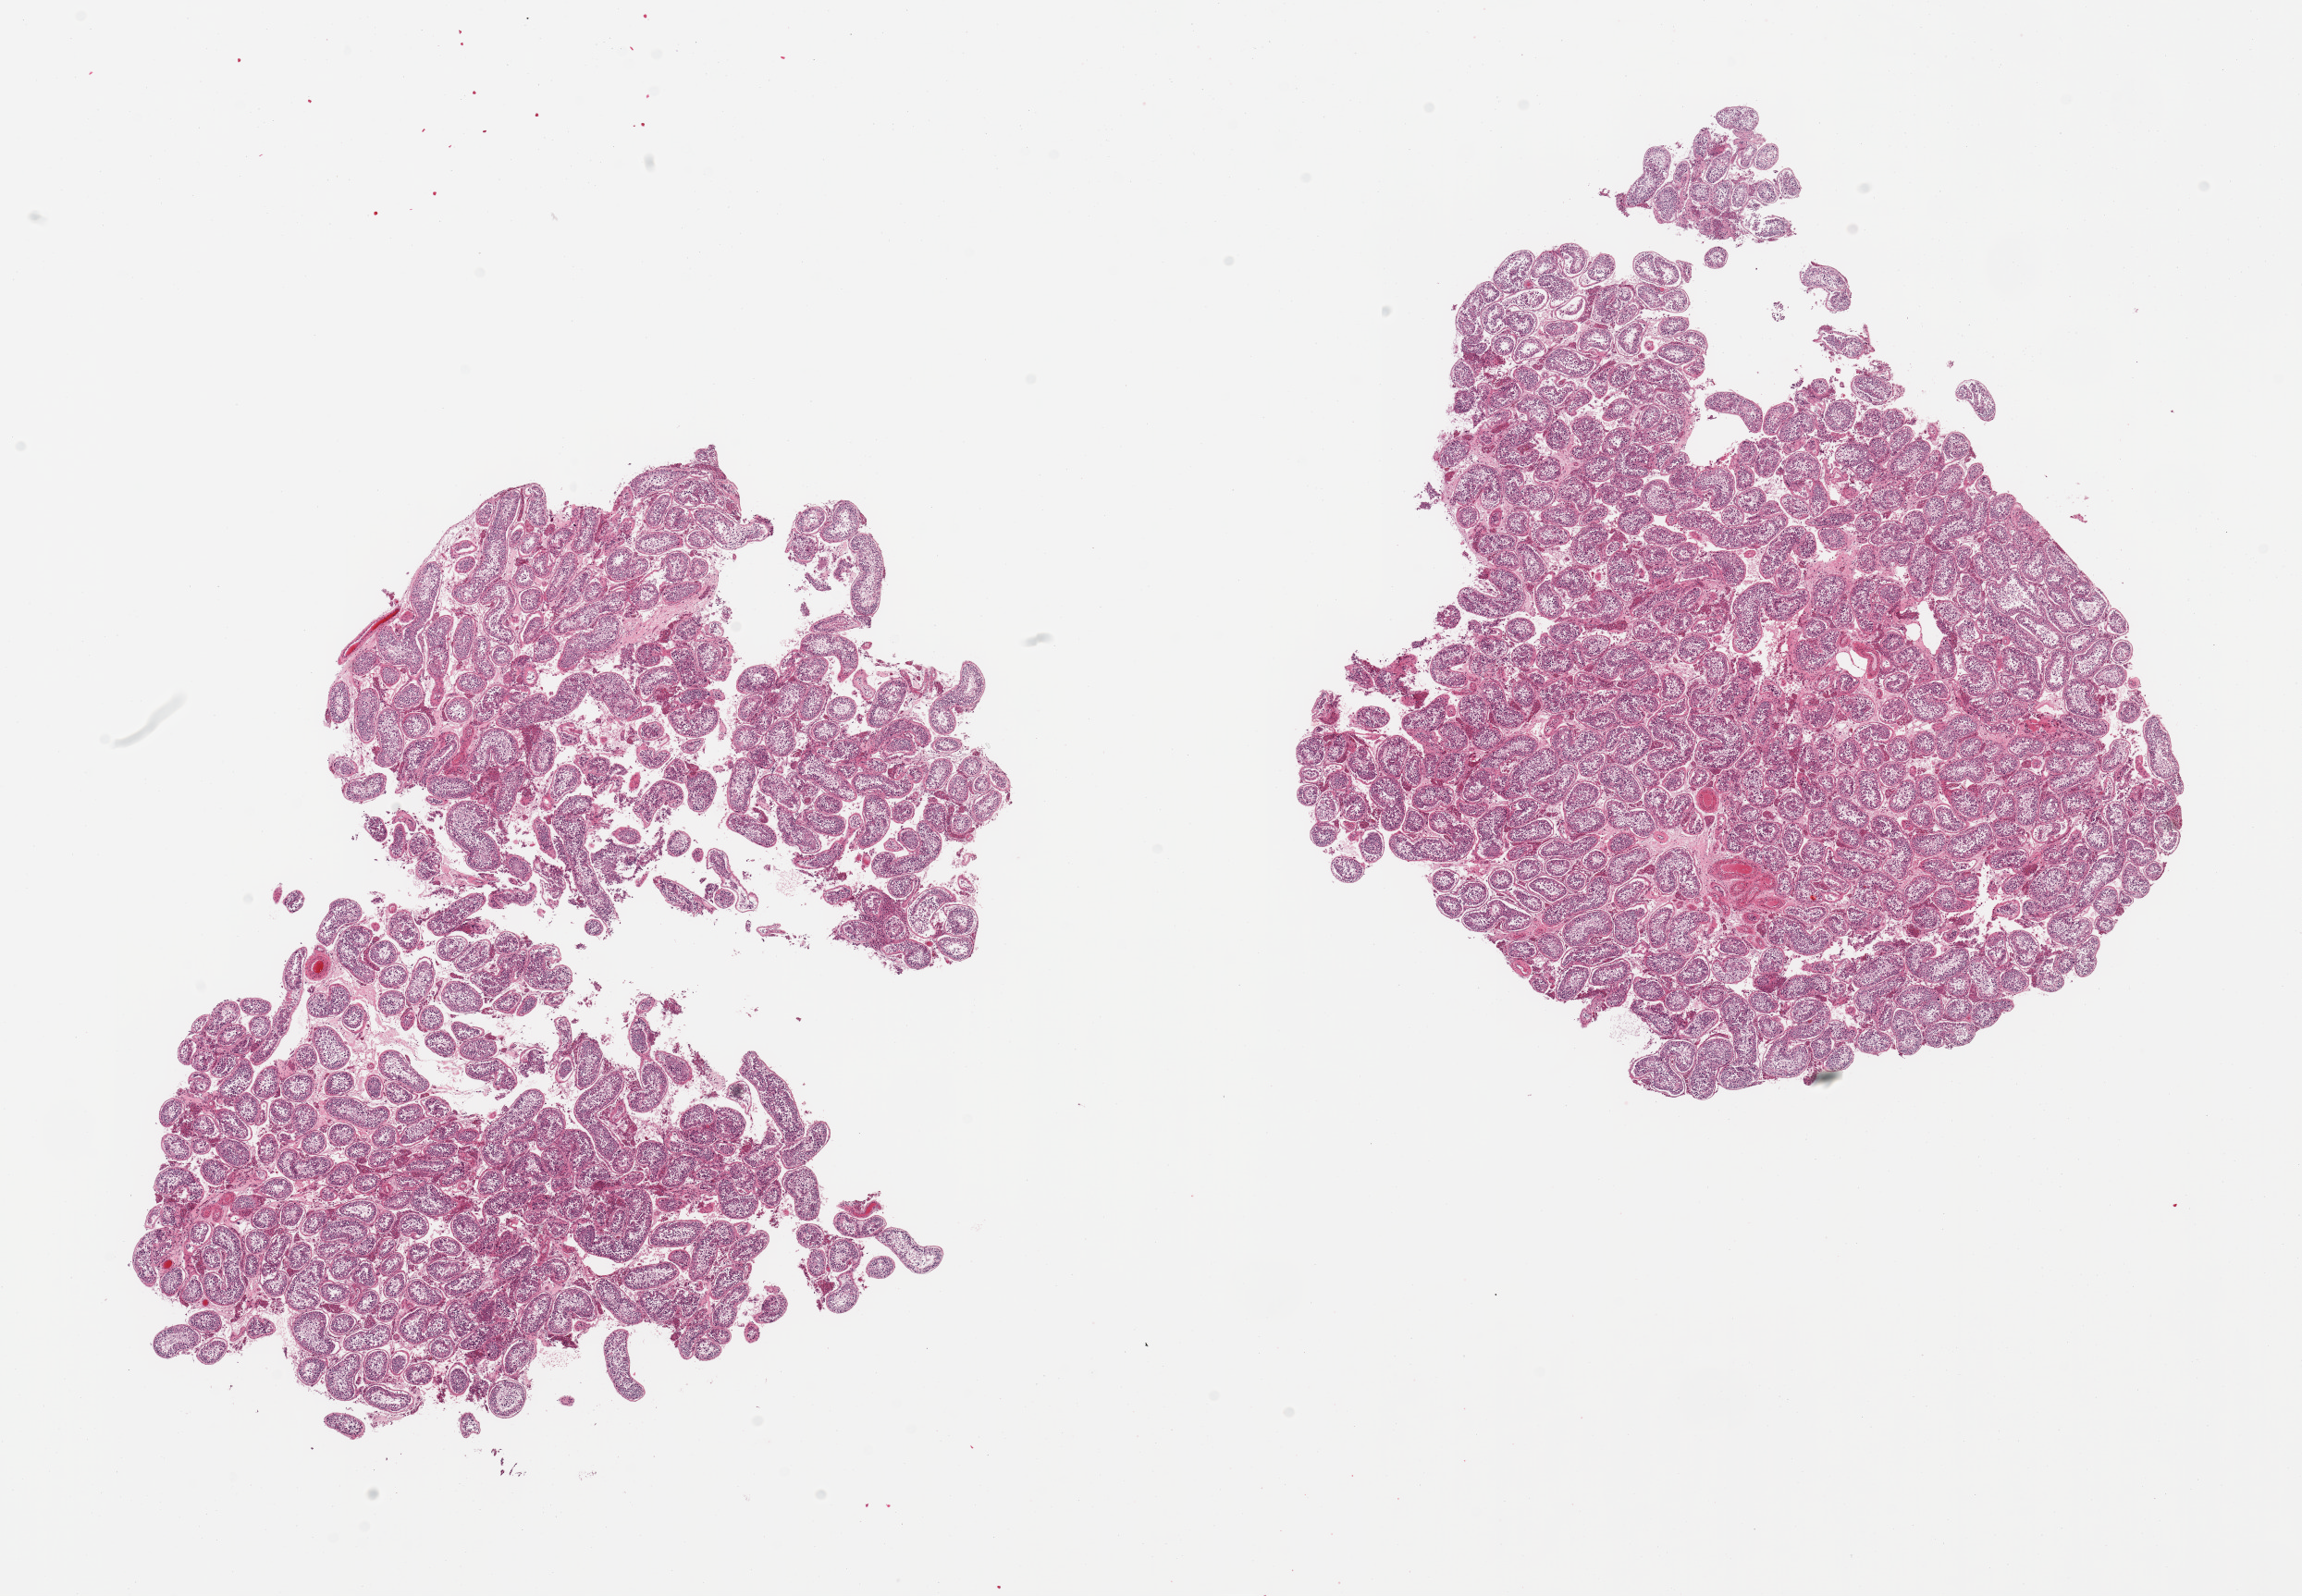
H&E whole-slide image — whole scanned area (about 19.7 x 13.7 mm) shown as a low-resolution overview; PAXgene-fixed paraffin-embedded (PFPE) section; section of testis (target tissue); donor tissue sample. Donor sex: male.
Pathologist's review note for this sample: 2 pieces, spermatogenesis present but appears reduced.